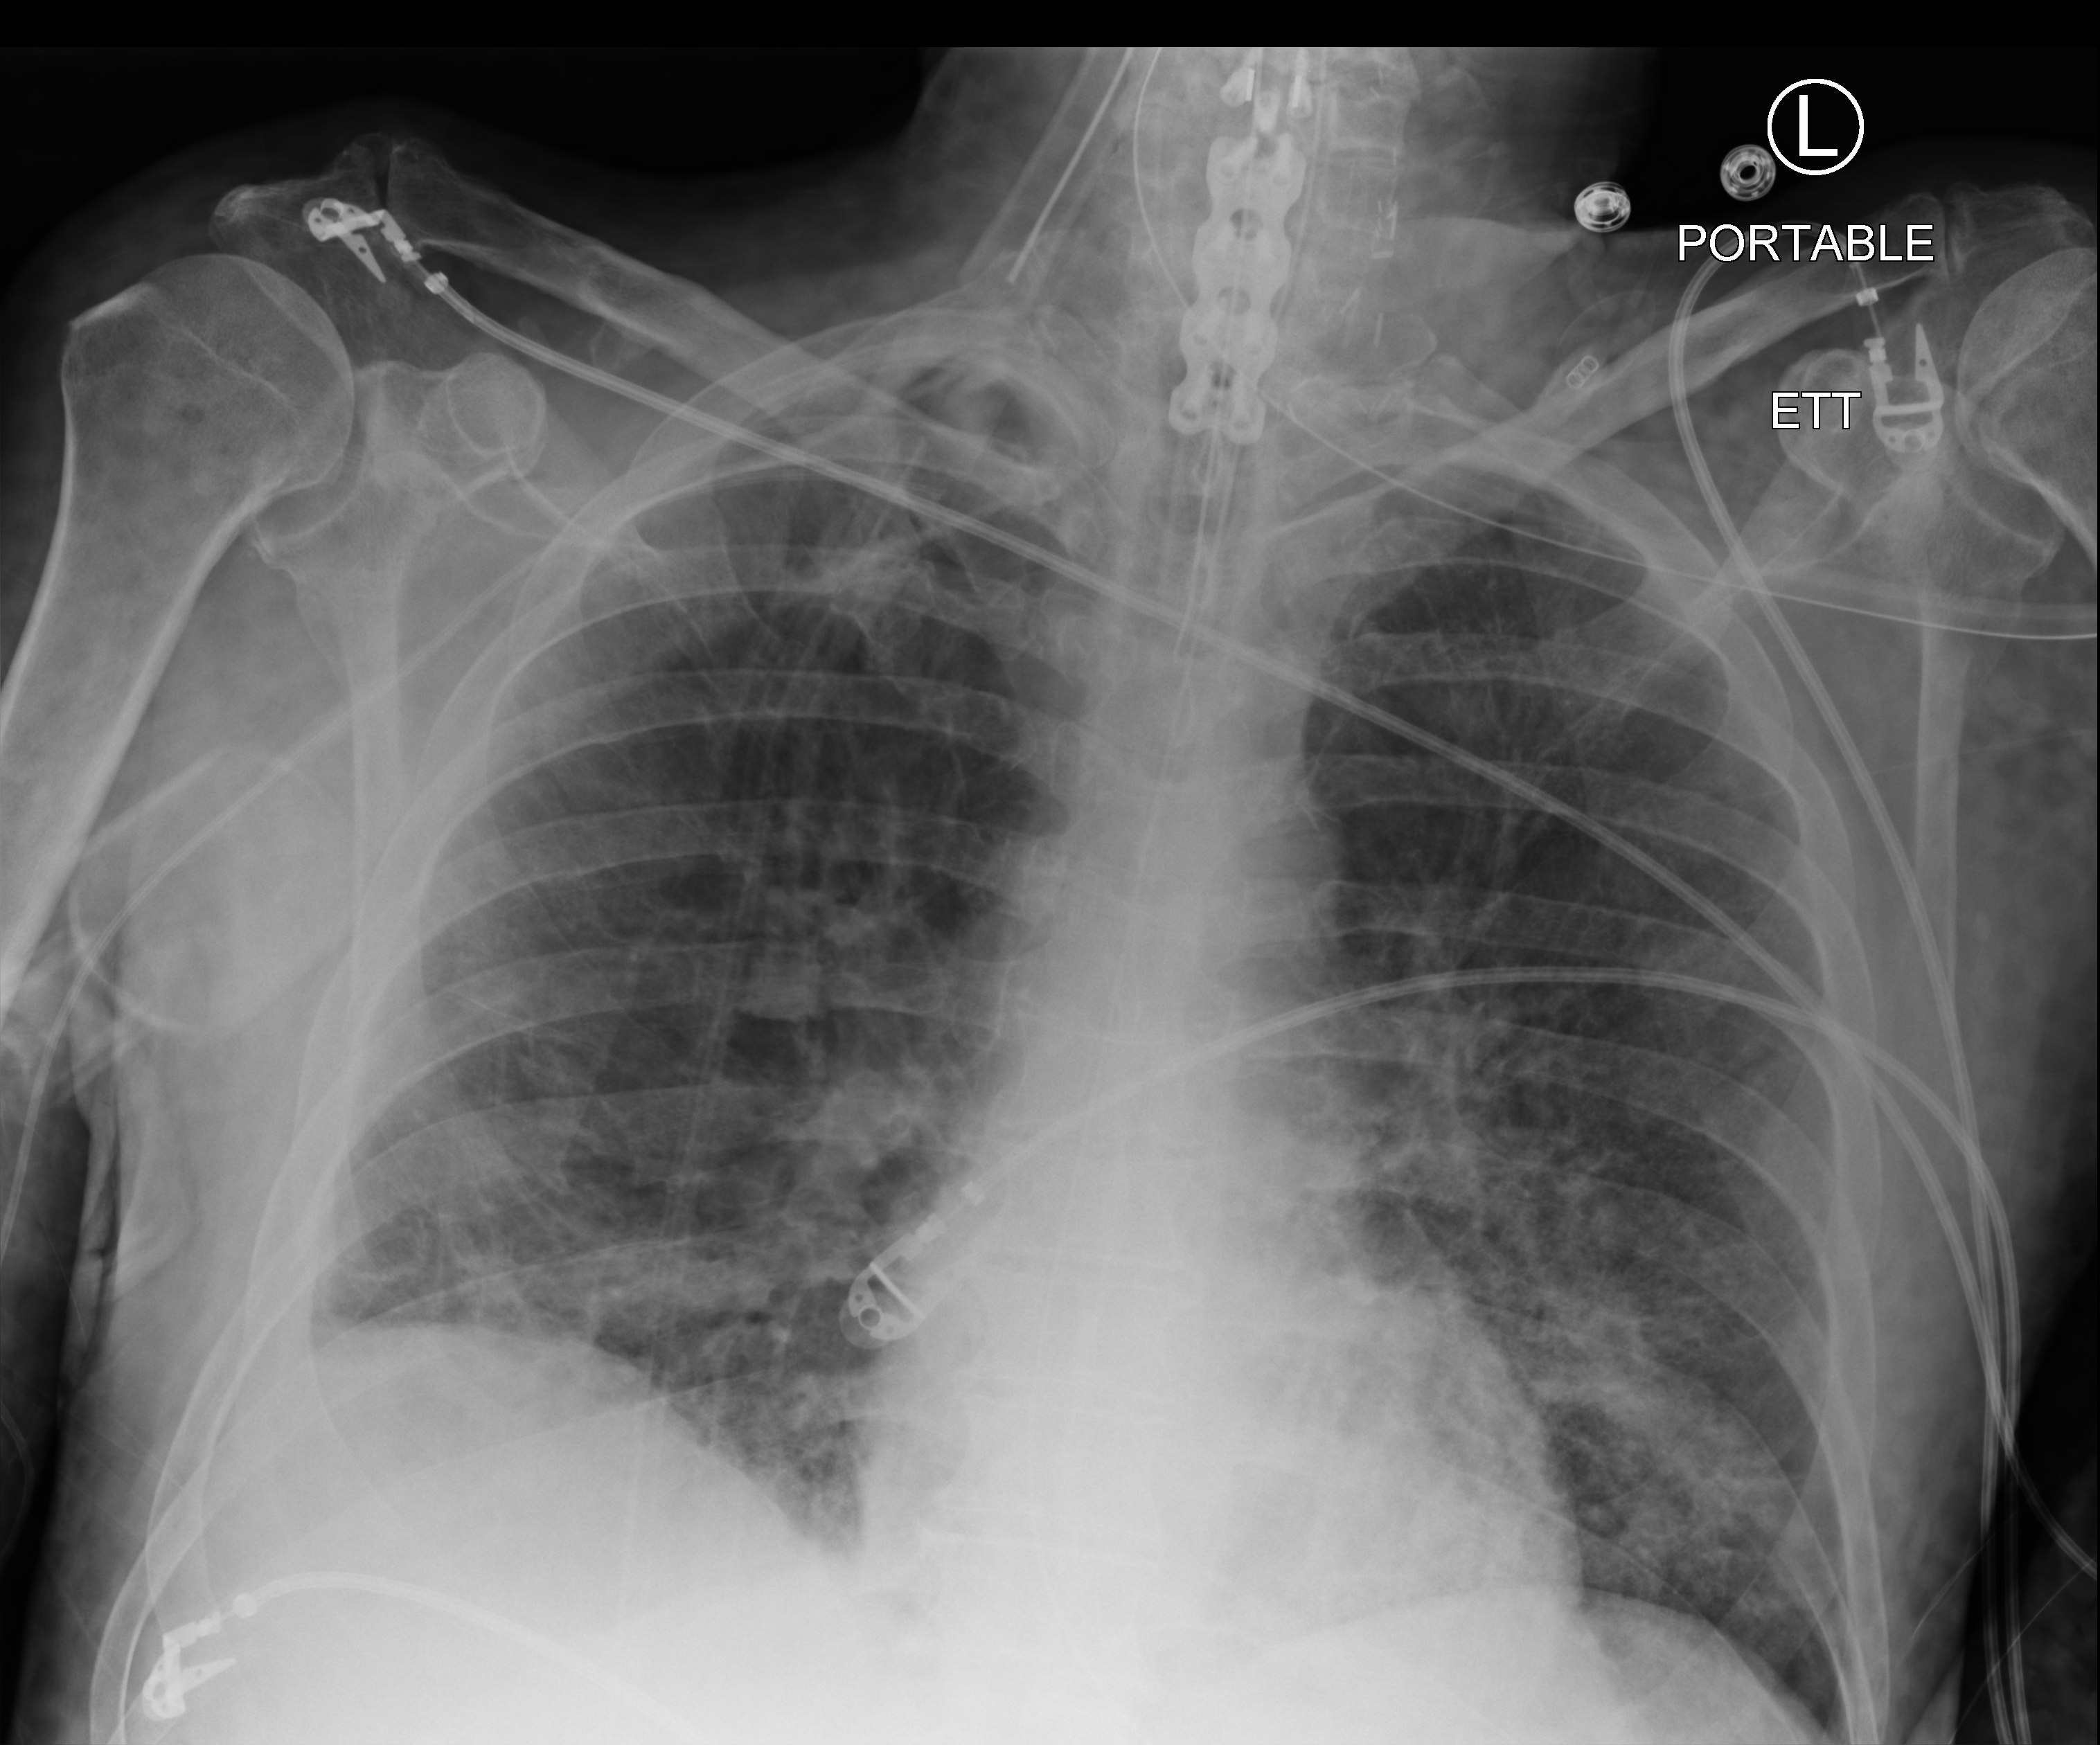
Bedside chest radiograph (computed radiography), anteroposterior (AP) projection. Male patient hospitalised with COVID-19, age 60–74 years.
Hospital-stay facts (about this admission, not read from this image; timing relative to this image not recorded):
- mechanically ventilated during this hospital stay: yes